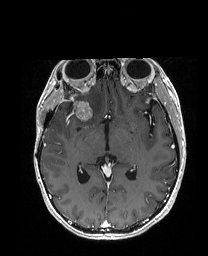
Brain MRI from a brain-tumour surgery series, one axial slice. Slice 99 of 192 in the series (ordered by position). T1-weighted post-contrast. 208 × 256 image matrix, field of view 203 × 250 mm. From the clinical record (not read from this slice): histopathology: Metastatic Carcinoma from Breast primary; tumour location: Right Frontal.
Structures marked on this image (manually delineated by an expert):
- previous resection cavity: box from (x=66, y=105) to (x=71, y=112) px
- tumour: (x=55, y=99)–(x=104, y=119)